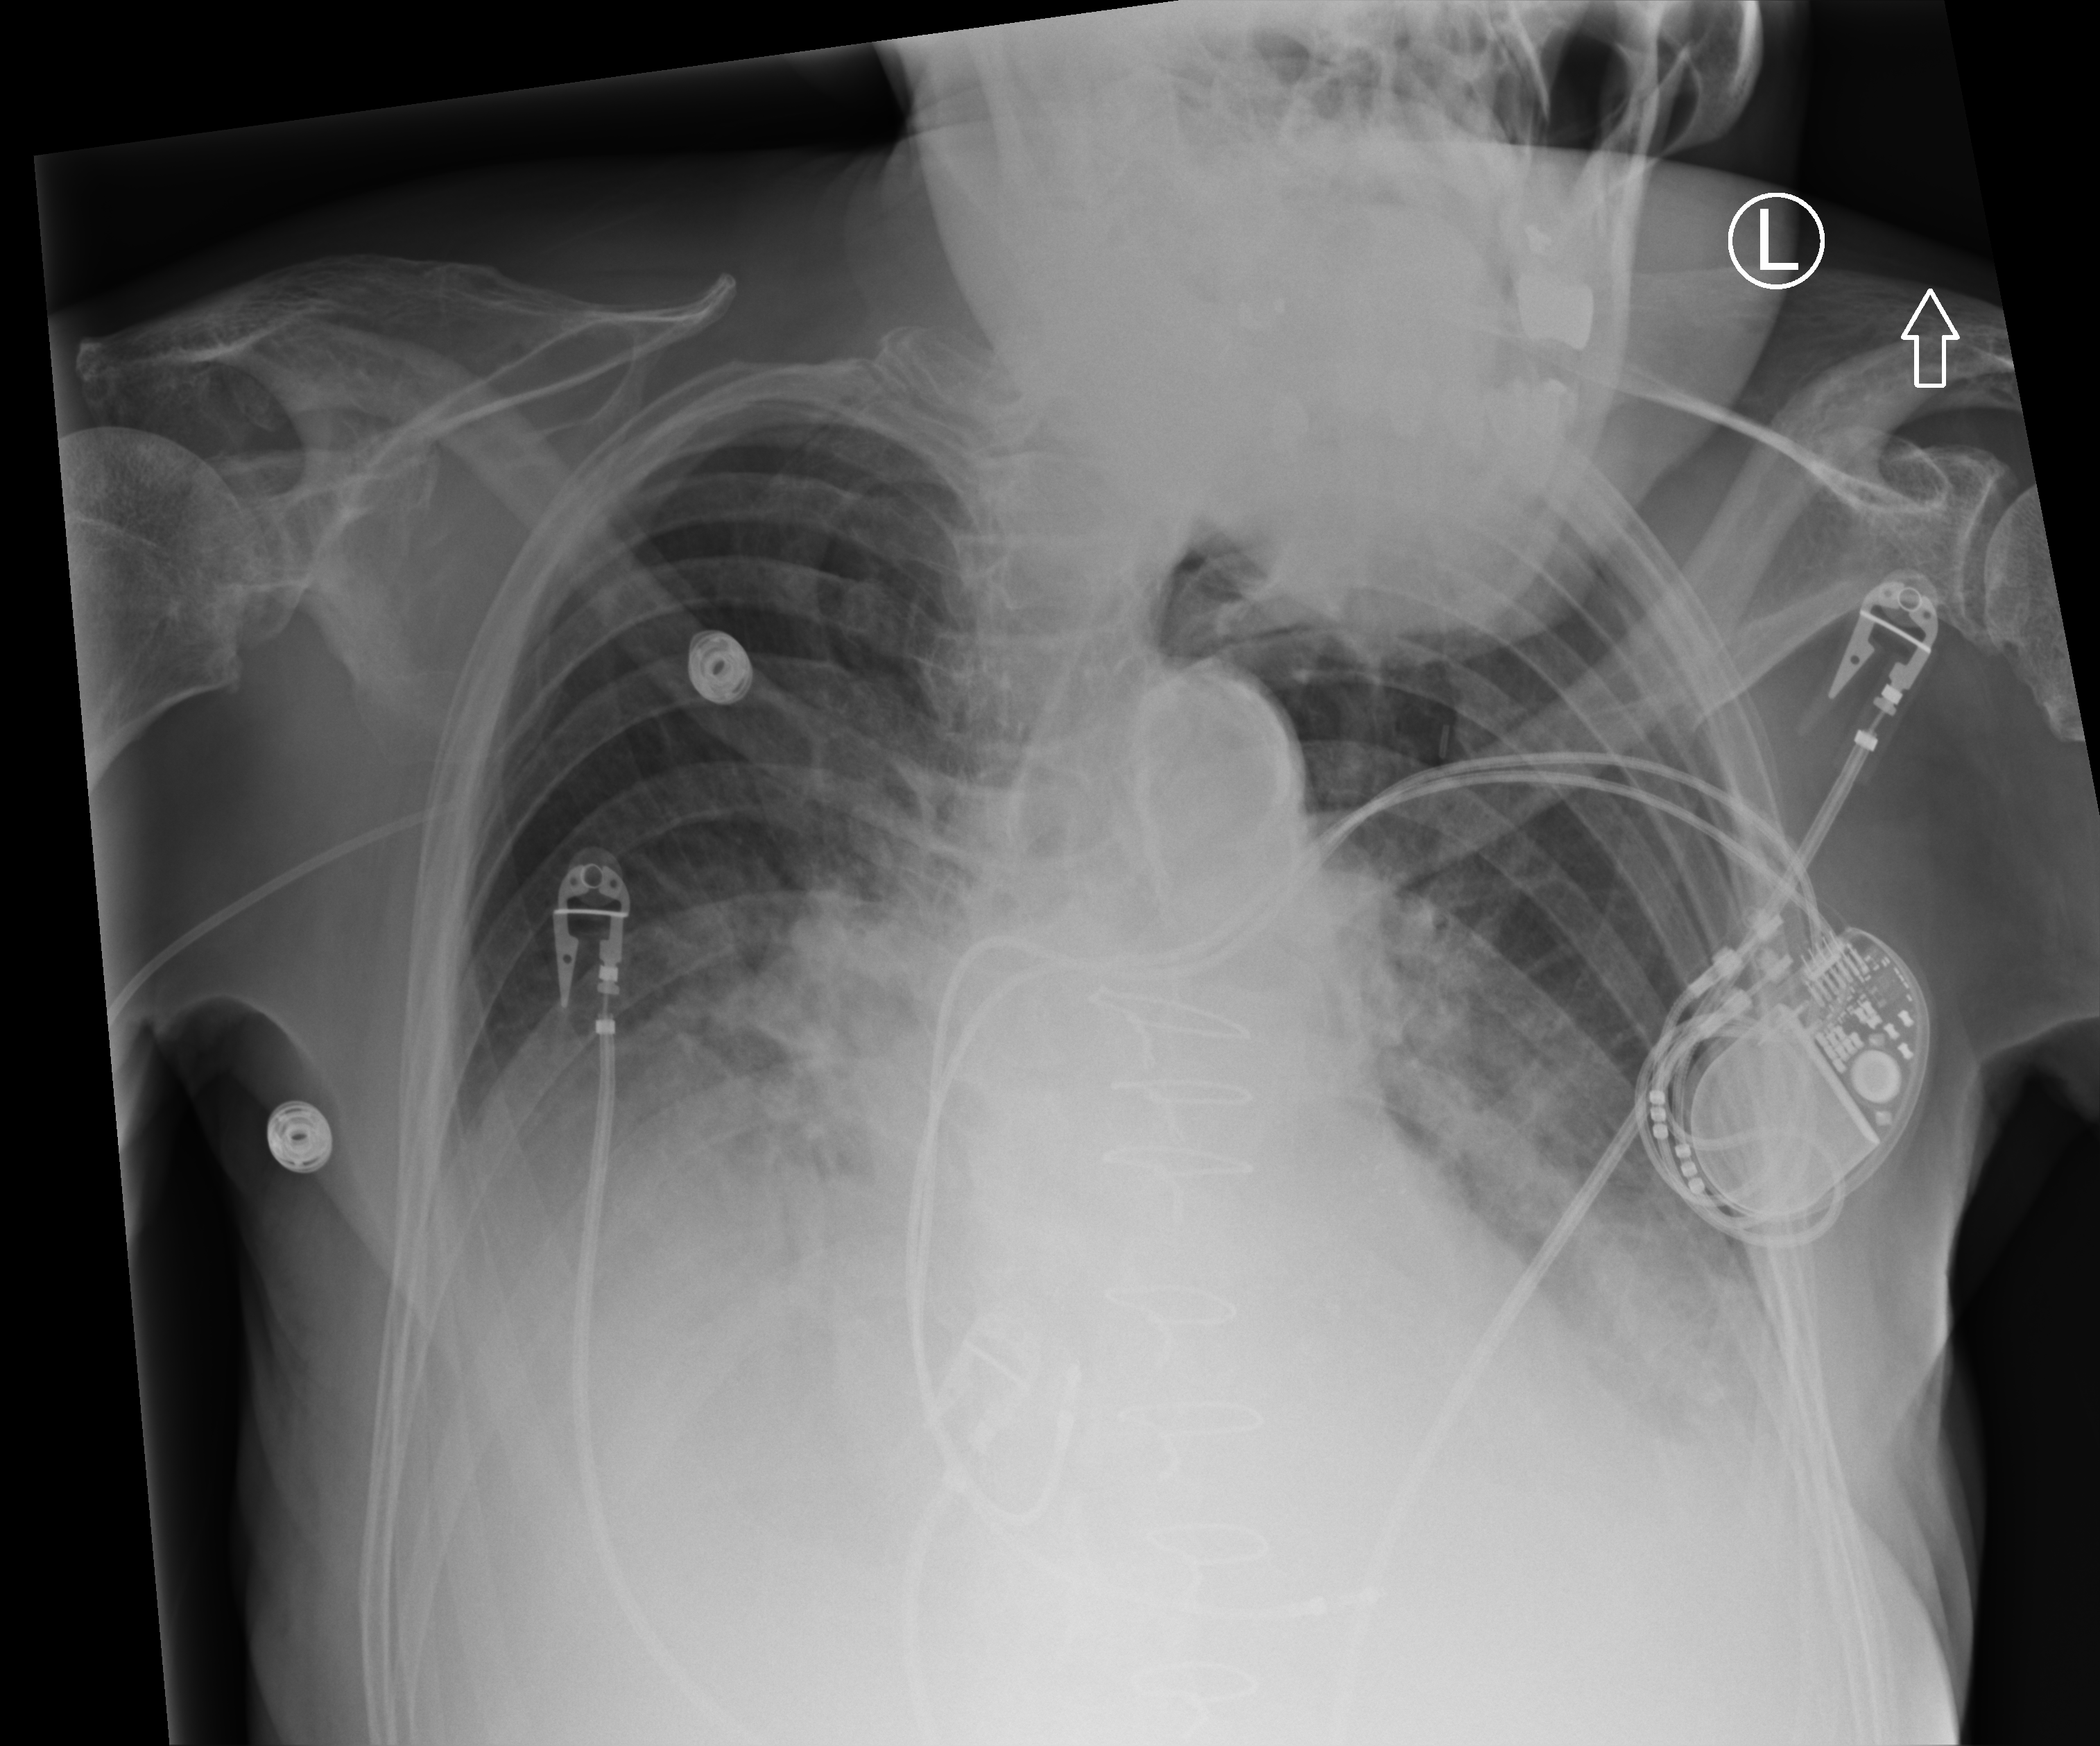
Bedside chest radiograph (computed radiography). Male patient hospitalised with COVID-19, age 60–74 years.
Admission-level facts for this patient (not findings on this image; timing relative to this image not recorded): admitted to intensive care during this hospital stay: no.